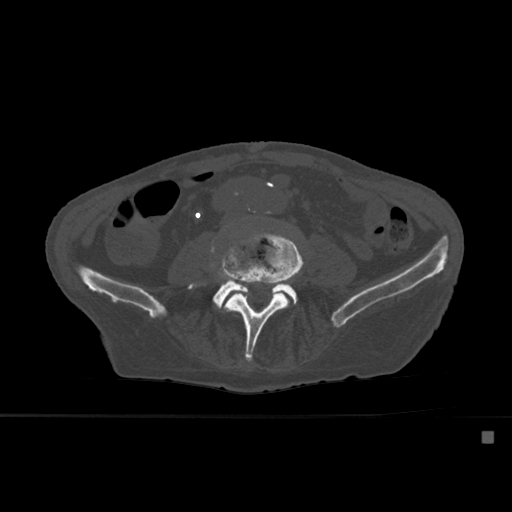
CT including the spine, one axial slice. Slice 189 of 527 in the series (ordered by position). Bone window (W 1800 / L 400 HU). 1.5 mm slice thickness. 512 × 512 image matrix, field of view 373 × 373 mm. Patient: male, 78 years. From the clinical record (not read from this slice): primary cancer: prostate.
Annotated regions visible in this slice (semi-automatic segmentation, software-assisted and operator-edited):
- L4 vertebra: bounding box [x1, y1, x2, y2] px = [214, 231, 303, 361]
- L5 vertebra: [191, 280, 298, 308]